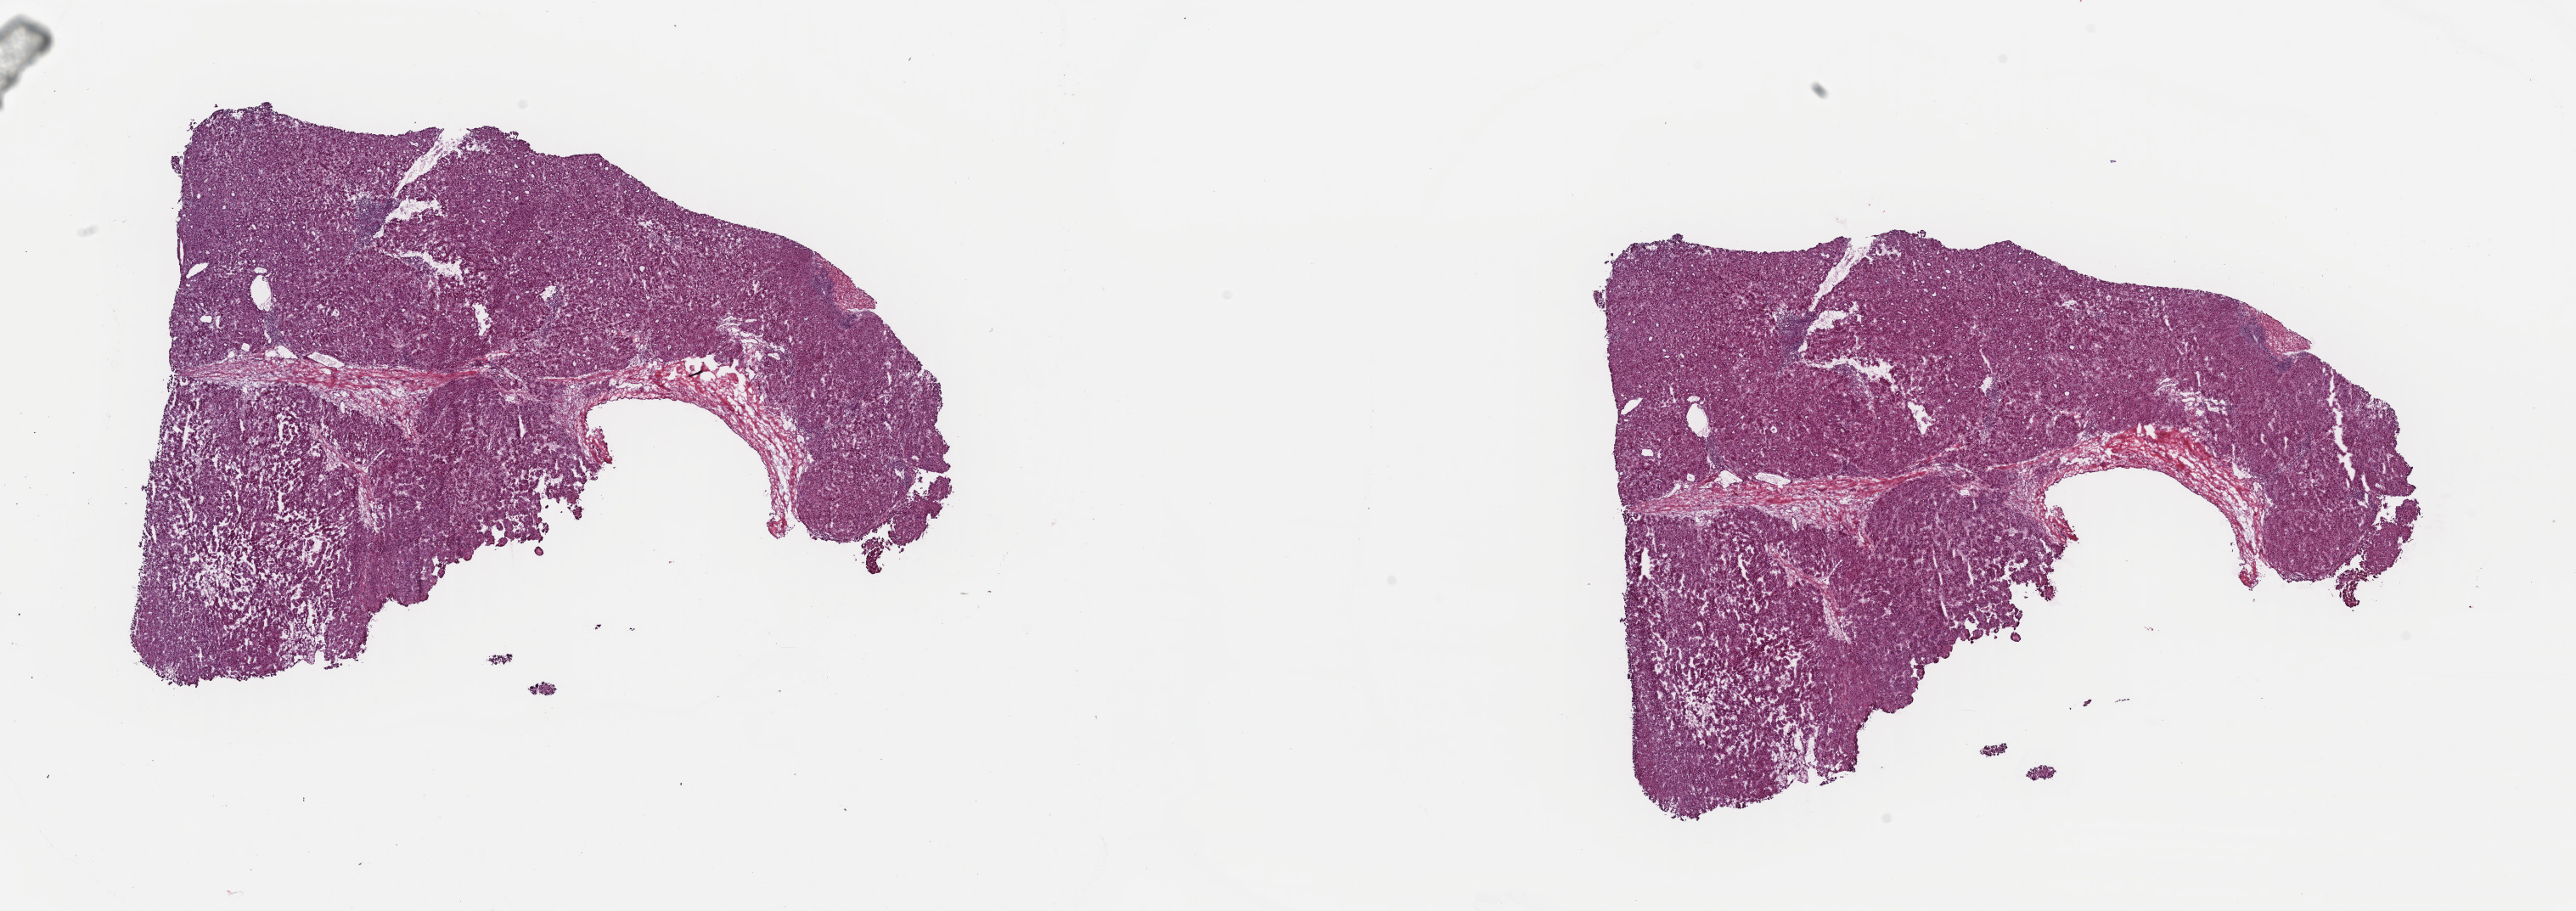
Digitized H&E-stained tissue section (whole slide) — a low-resolution overview of the entire scanned area, about 23.9 x 8.5 mm (from a 40x scan); frozen section from the top of the tissue portion; liver, primary tumour sample. Male, age 70 years at initial diagnosis. Histologic grade: G2 (moderately differentiated). Composition of this section per pathologist review: tumour cells 90%, tumour nuclei 90%, normal cells 0%, stromal cells 10%, necrosis 0%. Inflammatory infiltration, as recorded: lymphocyte infiltration 0%, monocyte infiltration 0%, neutrophil infiltration 0%.
AJCC pathologic stage: II. Pathologic diagnosis: Hepatocellular carcinoma, NOS.